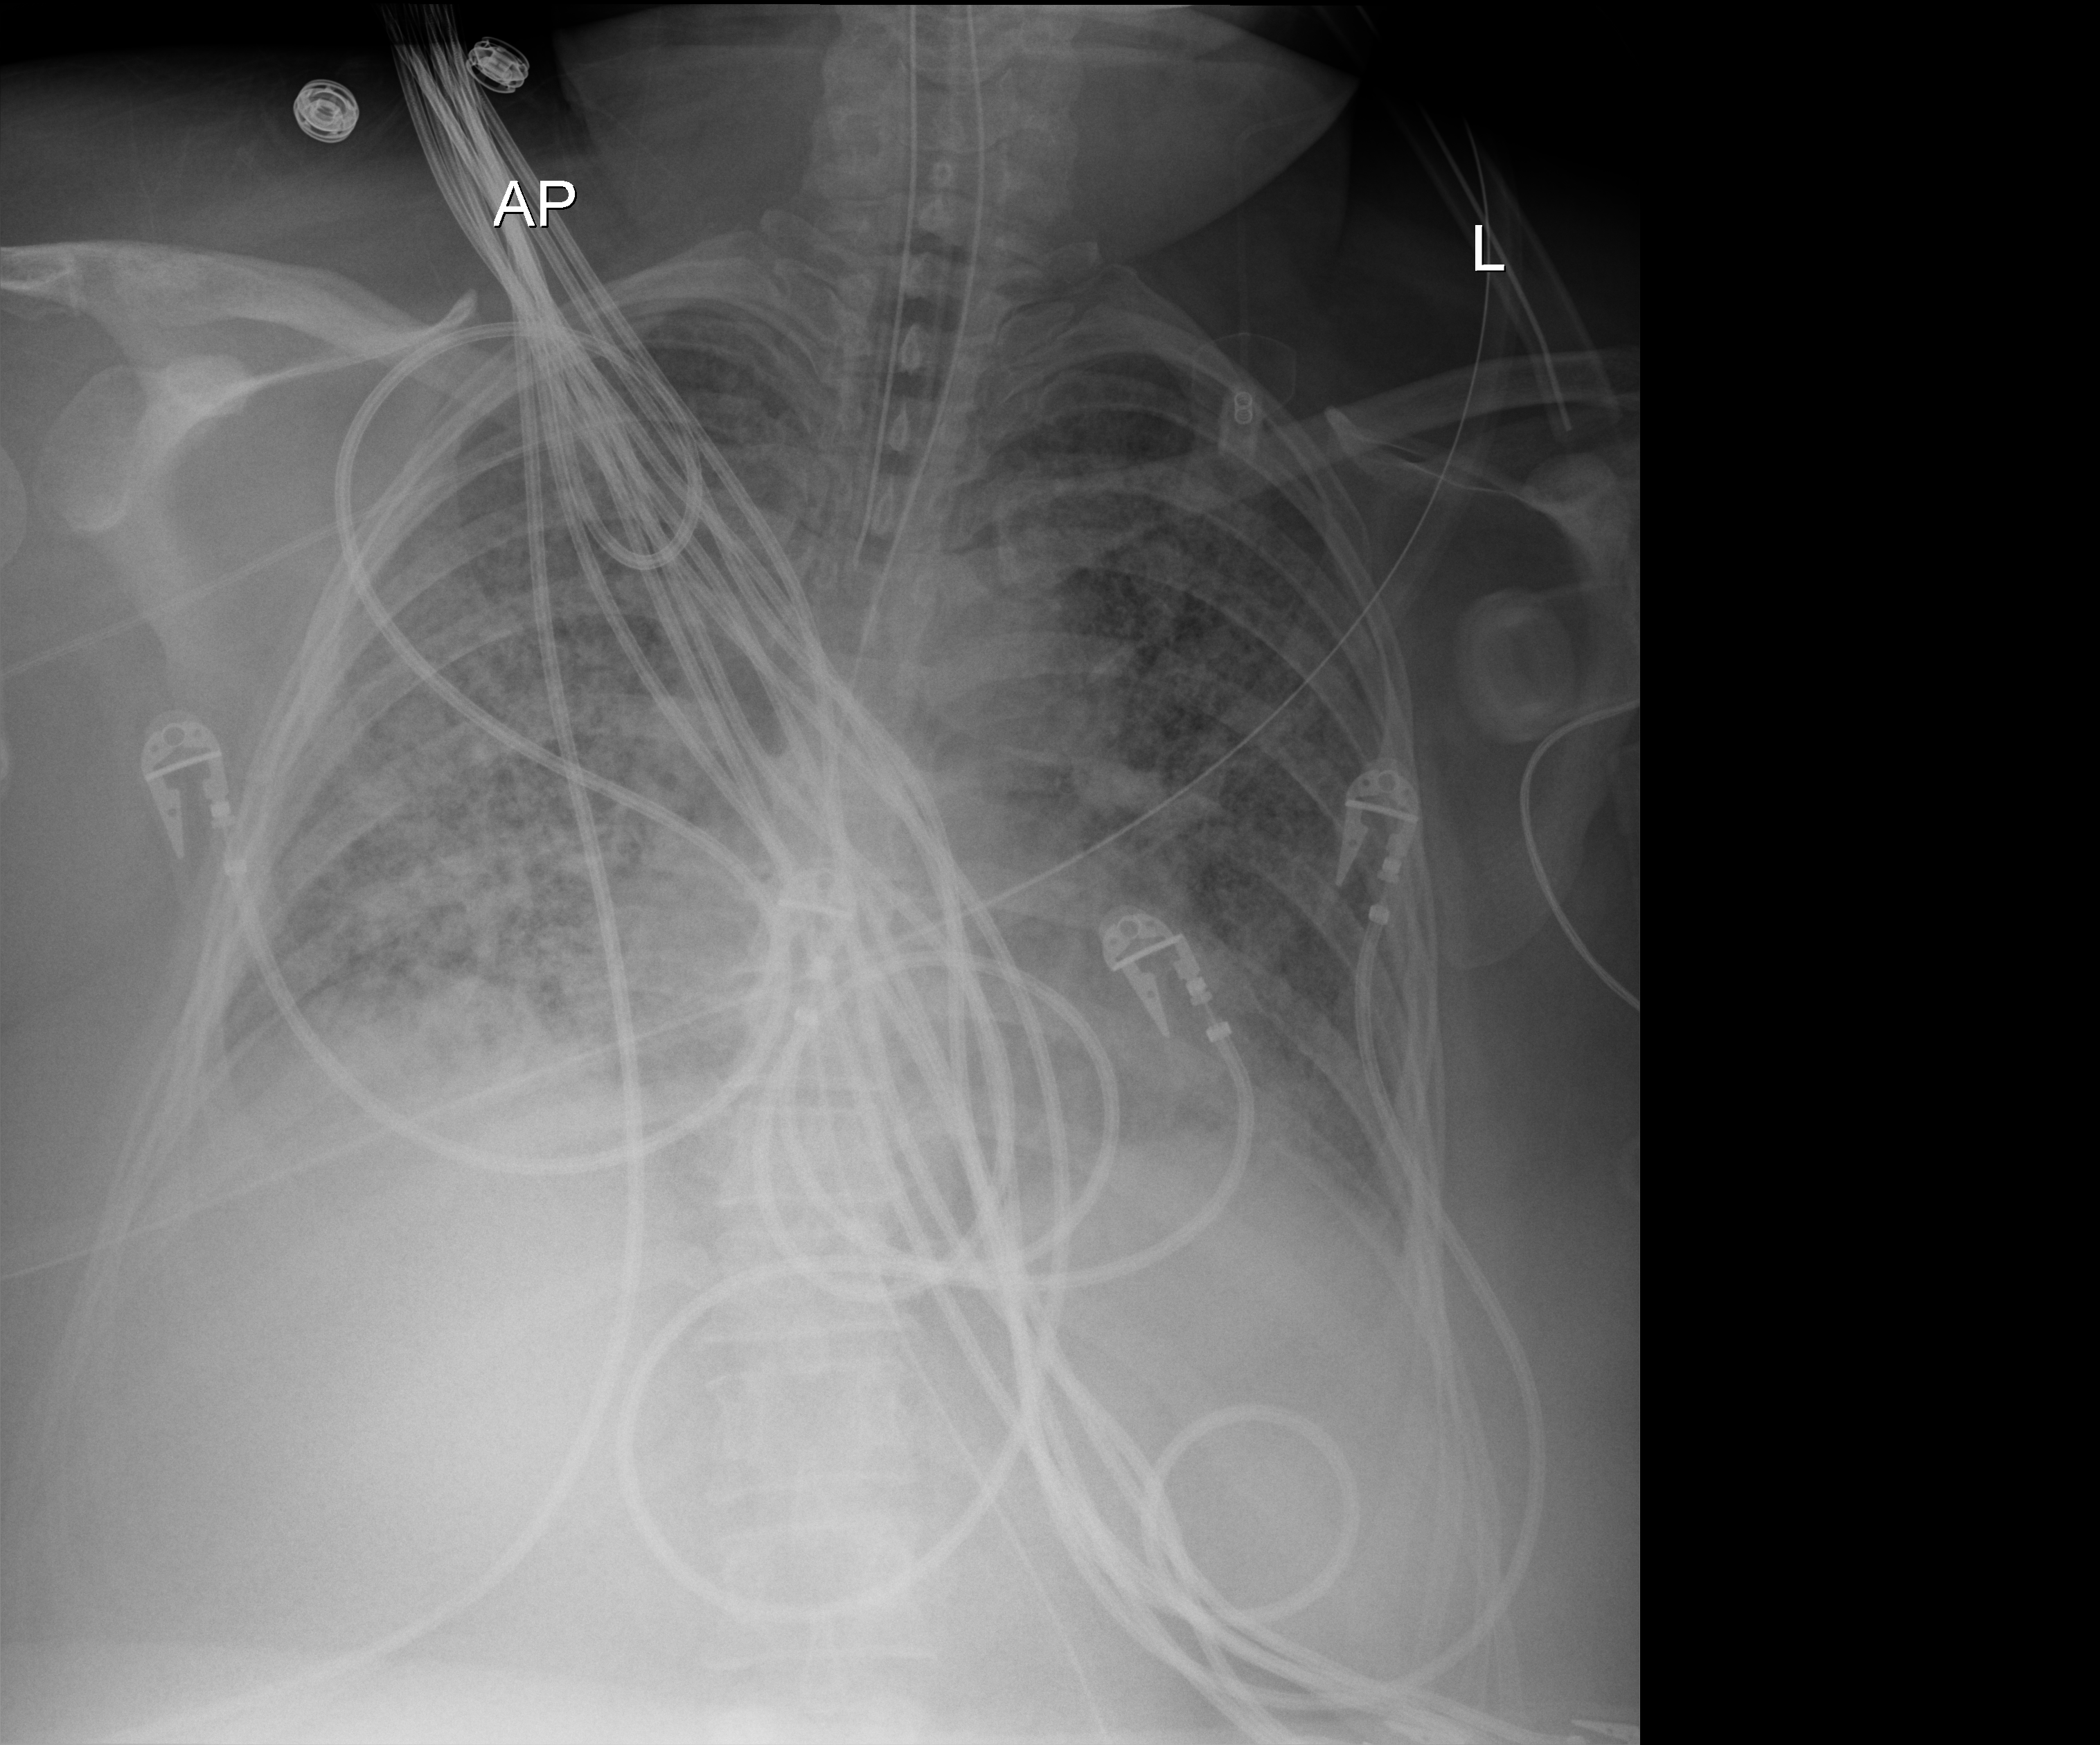
Portable chest radiograph, anteroposterior (AP) projection. Female patient hospitalised with COVID-19, age 18–59 years.
Admission-level facts for this patient (not findings on this image; timing relative to this image not recorded):
- mechanically ventilated during this hospital stay: yes